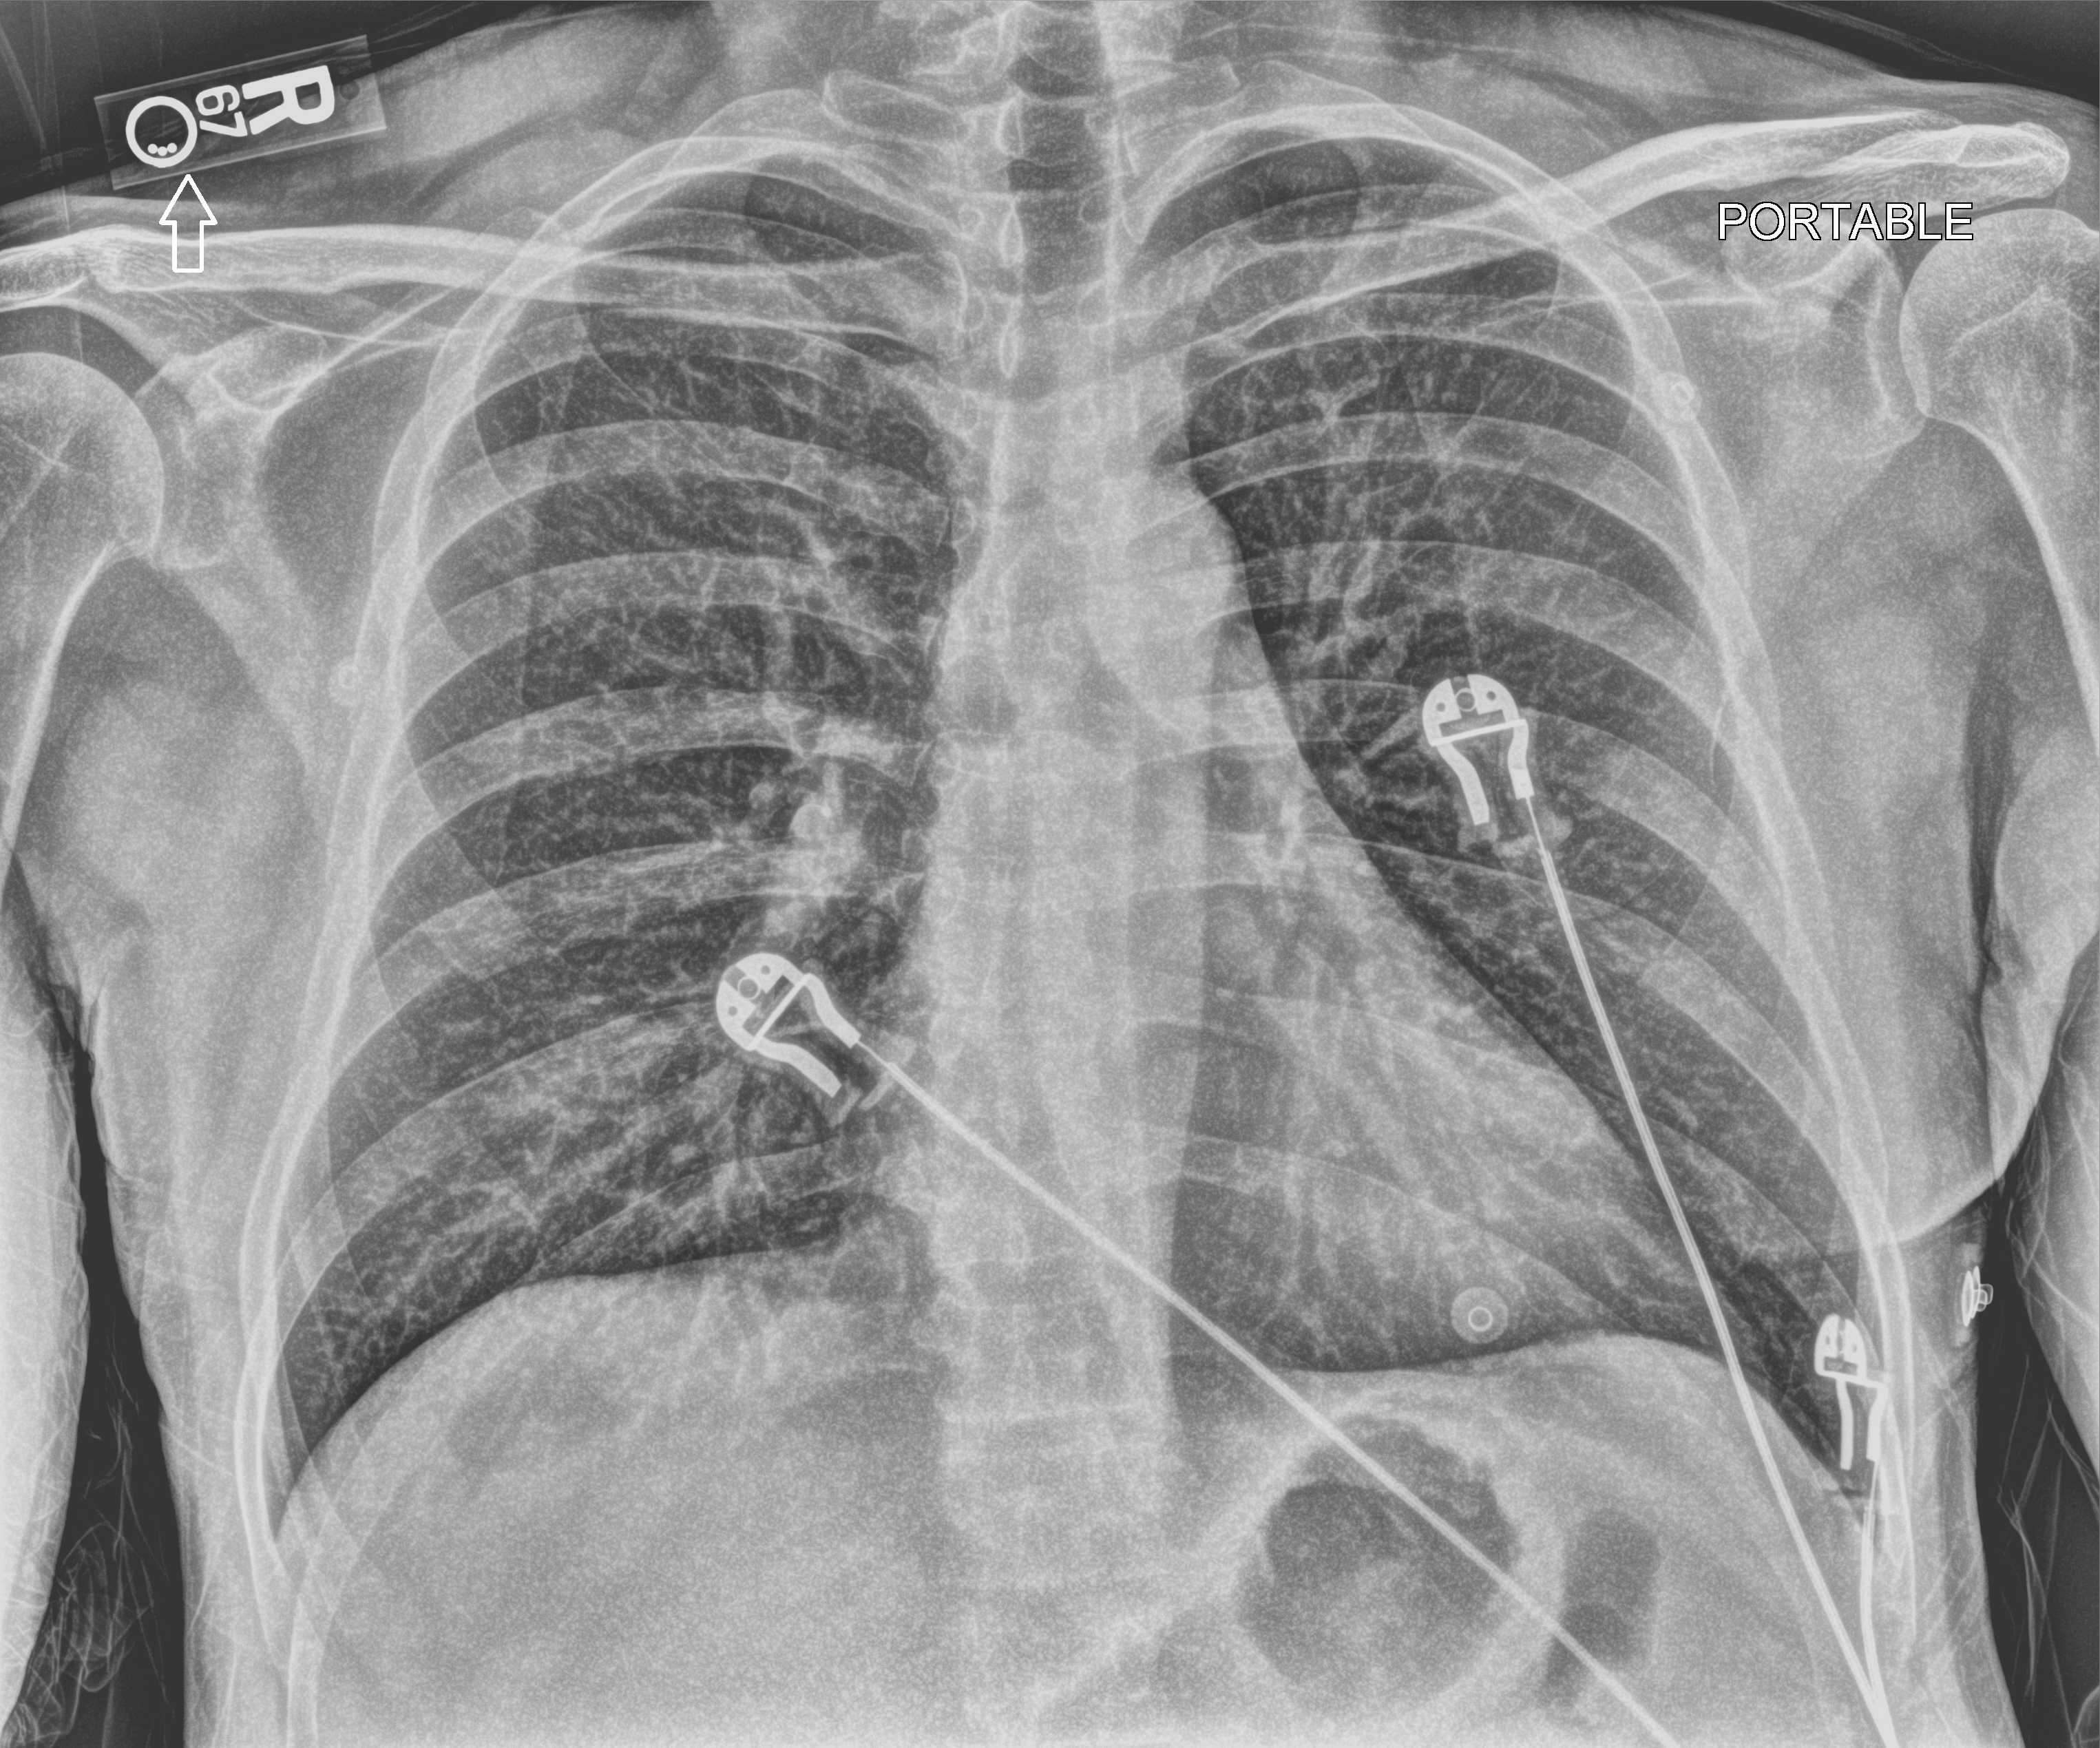
Chest X-ray (portable); anteroposterior (AP) projection. Male patient hospitalised with COVID-19, age 18–59 years.
From the hospital-stay record, not from the radiograph (when in the stay this image was taken is not recorded):
- chronic kidney disease (admission record): no
- admitted to intensive care during this hospital stay: no
- mechanically ventilated during this hospital stay: no